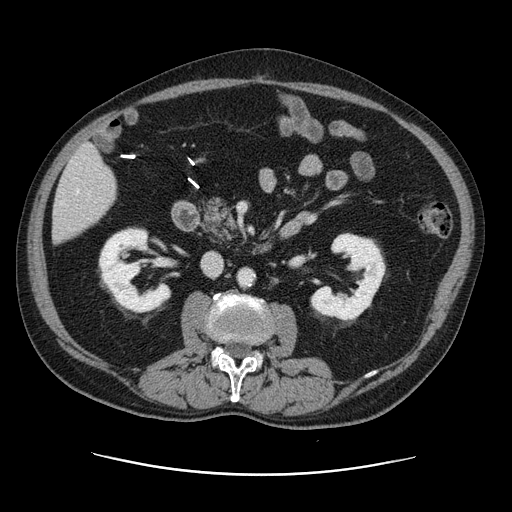
Contrast-enhanced abdominal CT, one axial slice; position 41 of 141 along the scan axis; 120 kVp; intravenous contrast given; soft-tissue window (W 400 / L 40 HU); 2.5 mm slice thickness; 512 × 512 image matrix, field of view 395 × 395 mm. Male patient, age 72 years. Case-level facts recorded for this patient, not image findings: diagnosis: colorectal cancer liver metastases, imaged before liver resection.
Structures marked on this image (expert manual segmentation):
- hepatic veins: bounding box (x1, y1, x2, y2) in pixels: (61, 189, 79, 204)
- liver: (54, 146, 117, 243)
- planned liver remnant (the part of the liver to remain after resection): (54, 149, 117, 243)